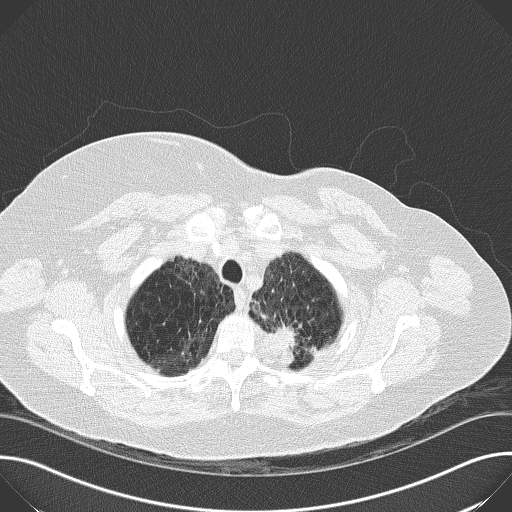
Low-dose screening chest CT, one axial slice; slice 148 of 169 in the series (ordered by position); reconstruction kernel B50f; lung window (W 1500 / L -600 HU); 2 mm slice thickness; 512 × 512 image matrix.
Structures marked on this image (expert manual segmentation):
- lesion 1 (tumor, upper lobe of left lung): bounding box <266,324,317,367> (left, top, right, bottom; pixels)